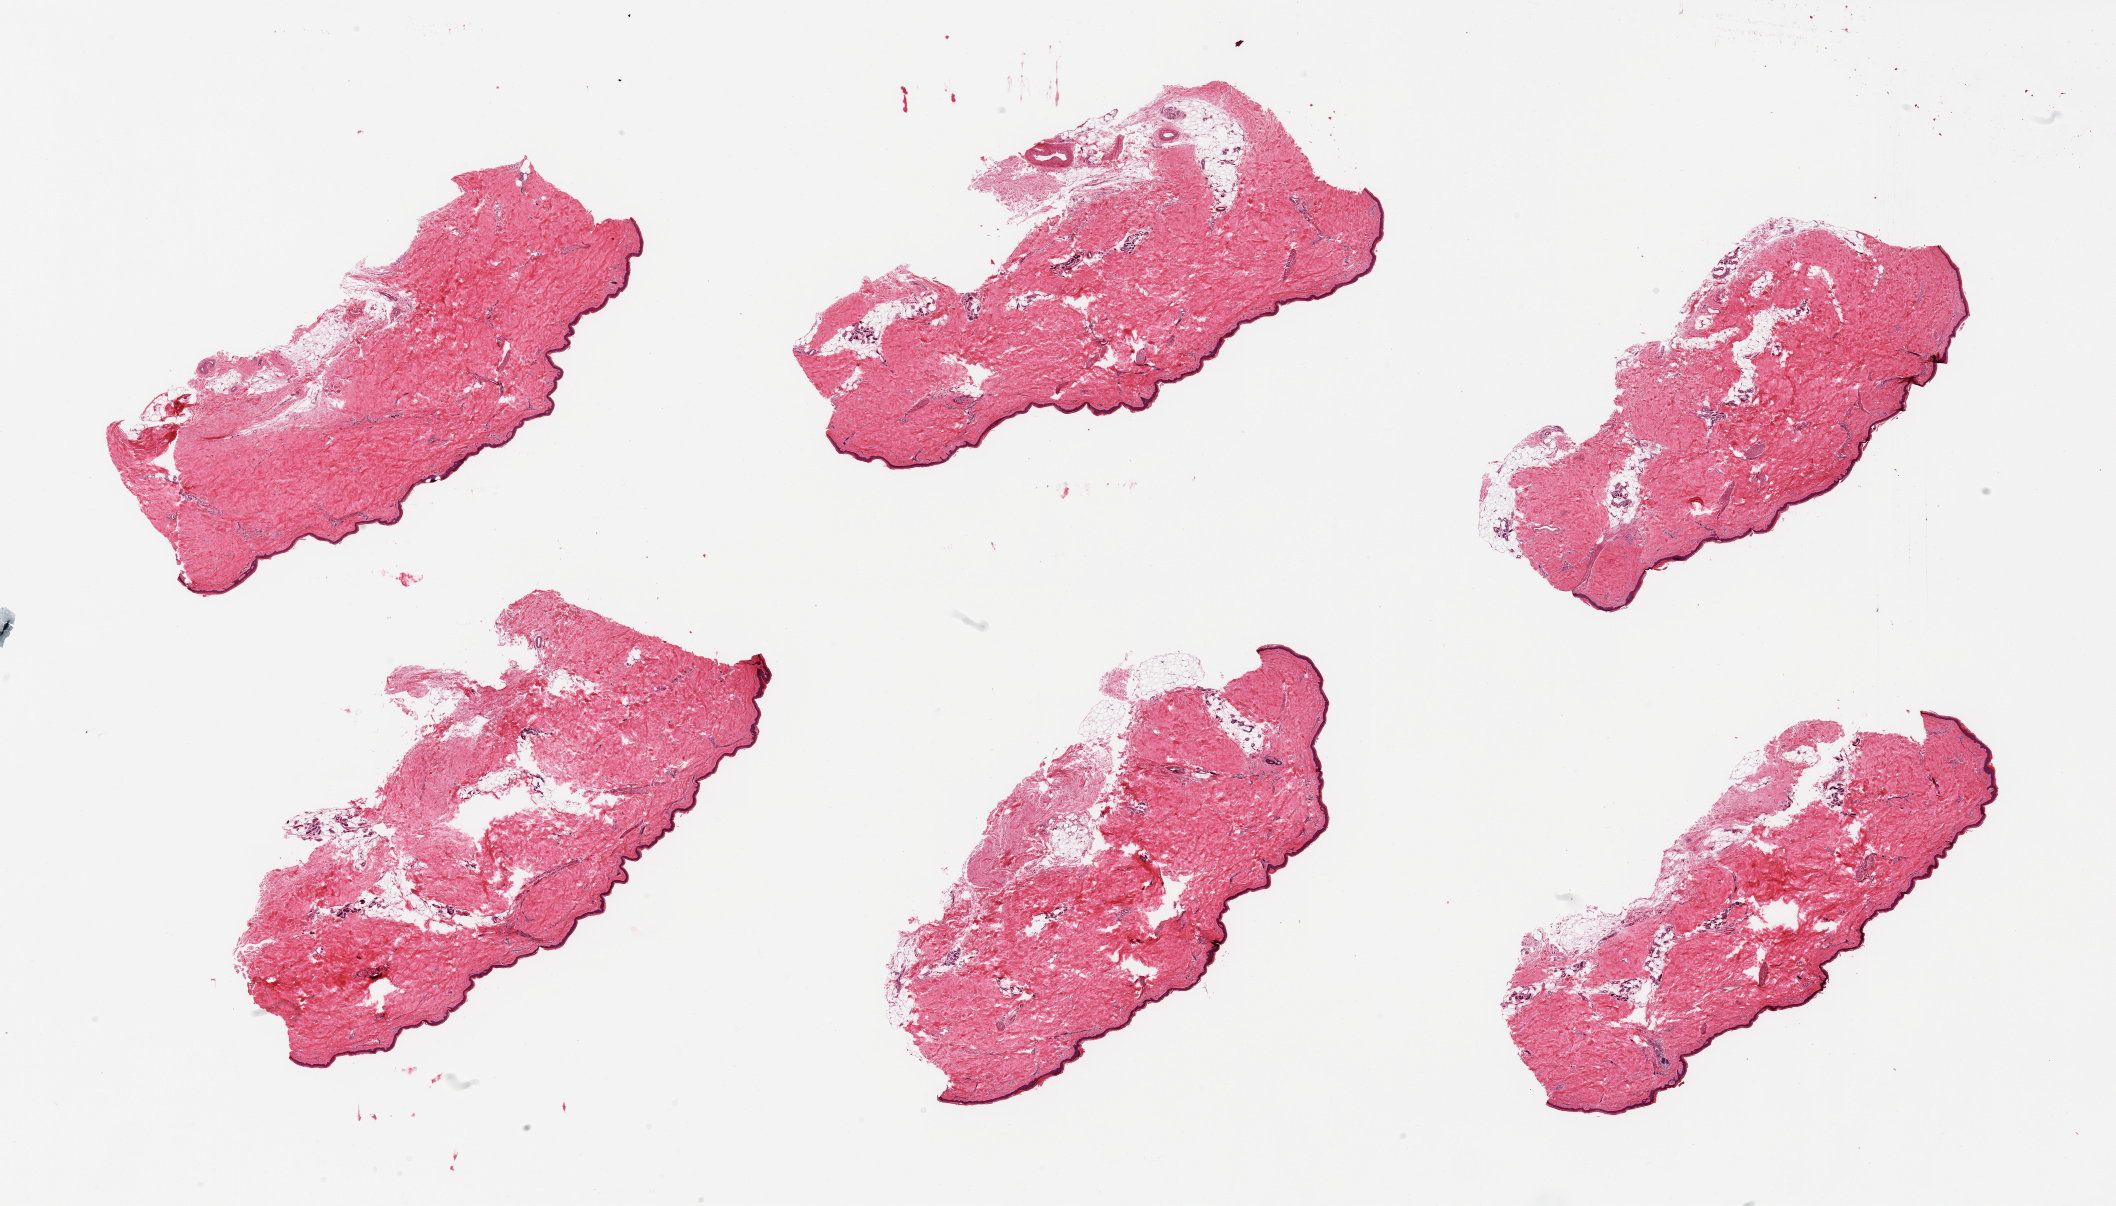
Digitized hematoxylin and eosin (H&E)-stained section, brightfield — low-resolution overview of the scanned area, about 33.5 x 19.1 mm; PAXgene-fixed, paraffin-embedded tissue; section of skin of lower leg (target tissue); donor tissue sample. Donor sex: male.
Reviewer comment on this tissue sample: 6 pieces, minimal adherent dermal fat; squamous epithelium is ~50 microns.